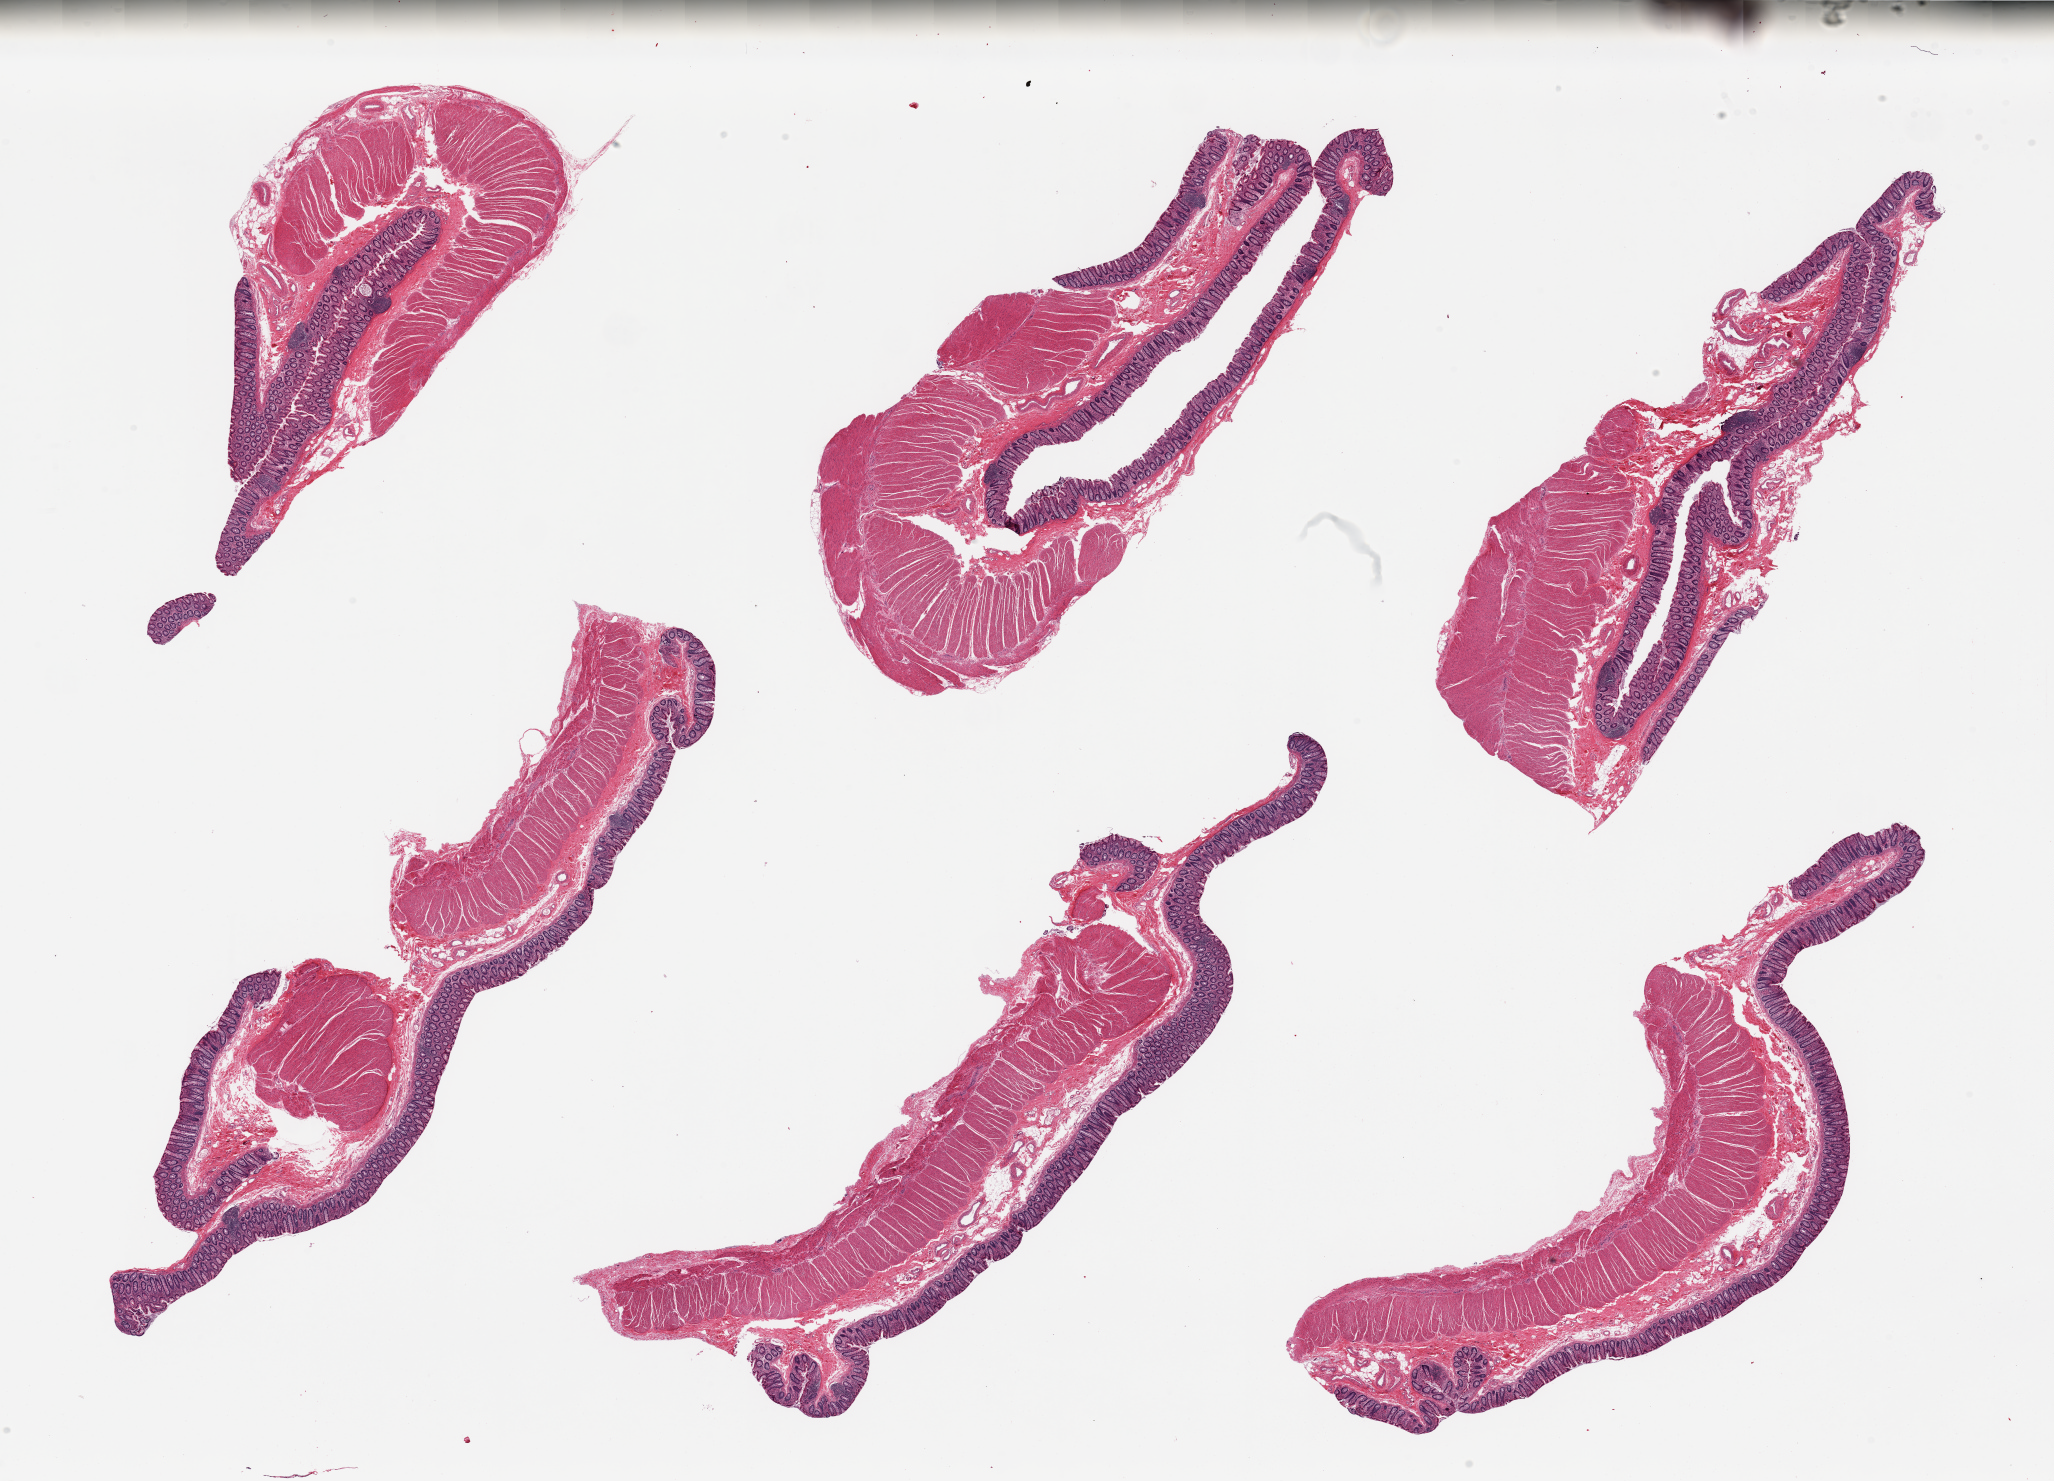
Haematoxylin and eosin whole-slide image — whole scanned area (about 32.5 x 23.4 mm, slide scanned at 20x) shown as a low-resolution overview; PAXgene-fixed, paraffin-embedded tissue; target tissue: transverse colon; tissue donor sample. Donor sex: female.
Reviewer comment on this tissue sample: 6 pieces, well dissected full thickness.